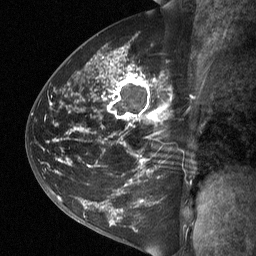
Breast MRI (dynamic contrast-enhanced), one sagittal slice; slice 35 of 64 in the series (ordered by position); dynamic contrast-enhanced study with each time point stored as its own series, time point 2 of 3 at this slice position (early post-contrast, ordered by acquisition time); 1.5 T; TE 4.8 ms, TR 27 ms; 256 × 256 image matrix, field of view 200 × 200 mm. Female patient, age 42 years. Case-level facts recorded for this patient, not image findings: setting: breast cancer imaged before/during neoadjuvant chemotherapy; receptor status: triple-negative.
Outlined on this slice (semi-automatically segmented with operator editing):
- analysis volume of interest (the breast-tissue region the enhancement analysis was run in; not a lesion): bounding box (x1, y1, x2, y2) in pixels: (49, 45, 196, 197)
- tumour enhancement mask (voxels above the 90 % enhancement threshold inside the analysis volume of interest): (111, 56, 168, 118)